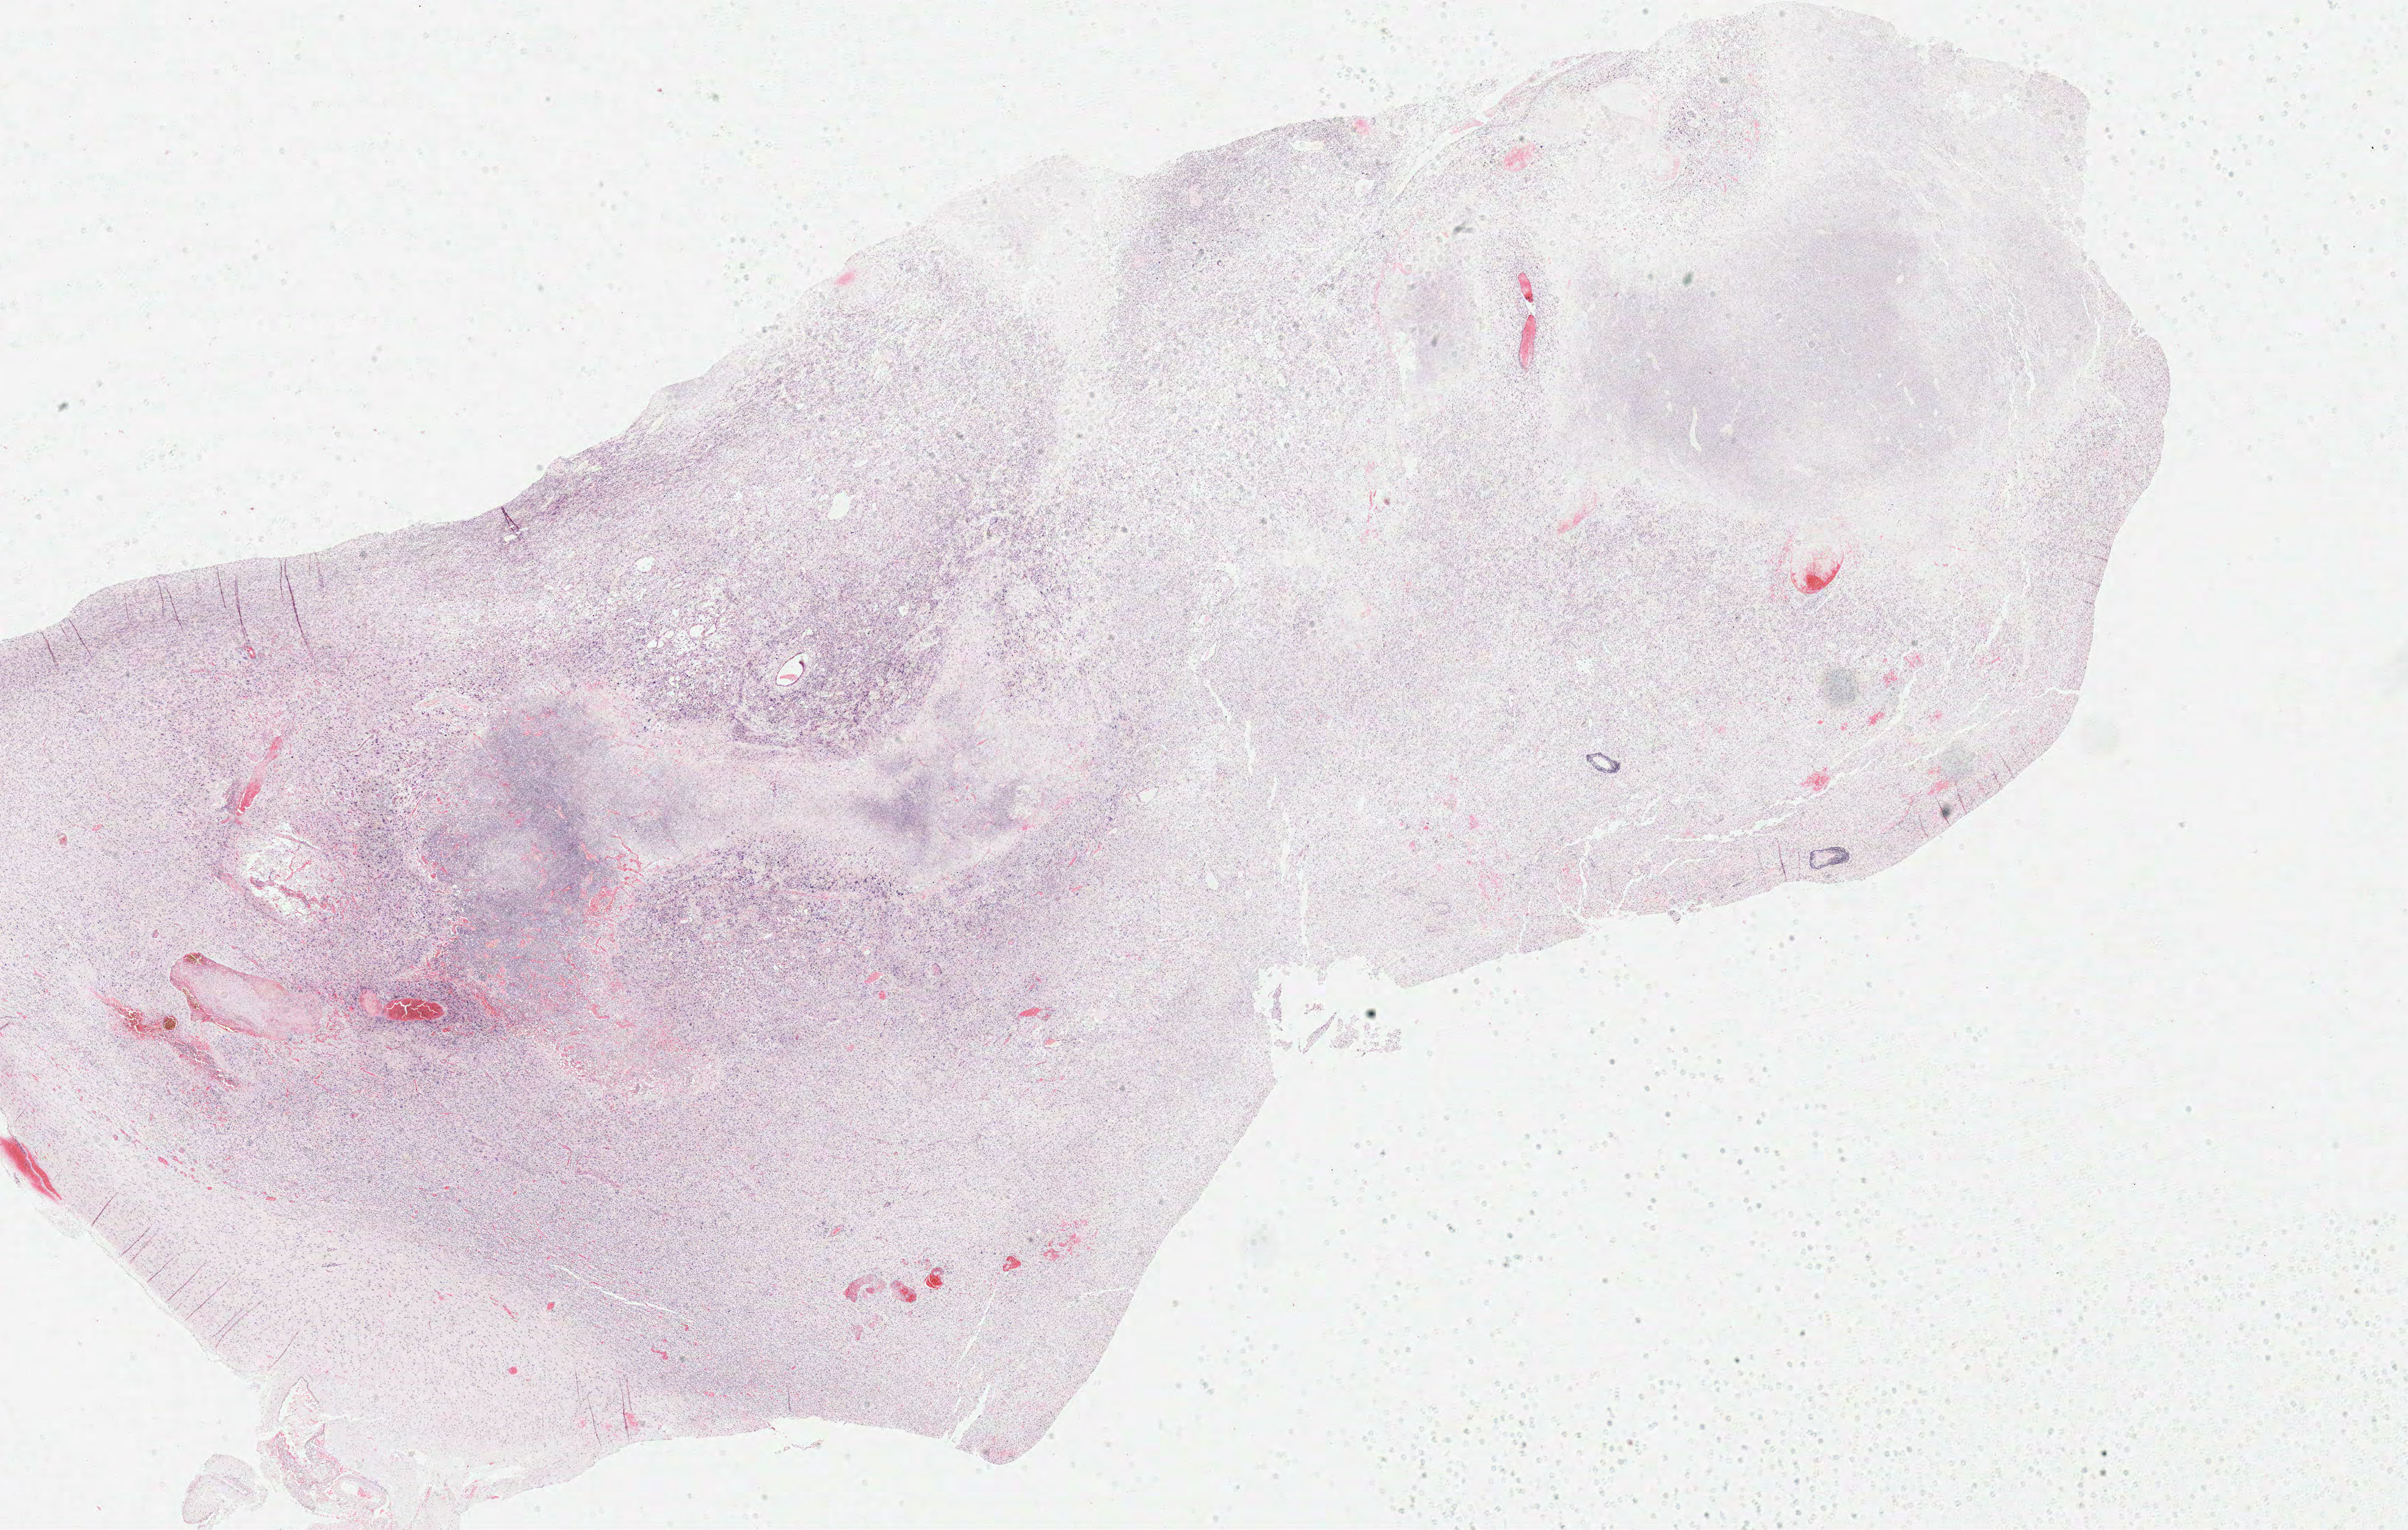
H&E whole-slide image — low-resolution overview of the scanned area, about 27.4 x 17.4 mm (slide scanned at 40x). Formalin-fixed paraffin-embedded (FFPE) diagnostic section. Primary tumour sample from the brain. Male patient; age at initial diagnosis 71 years.
• pathologic diagnosis: Glioblastoma